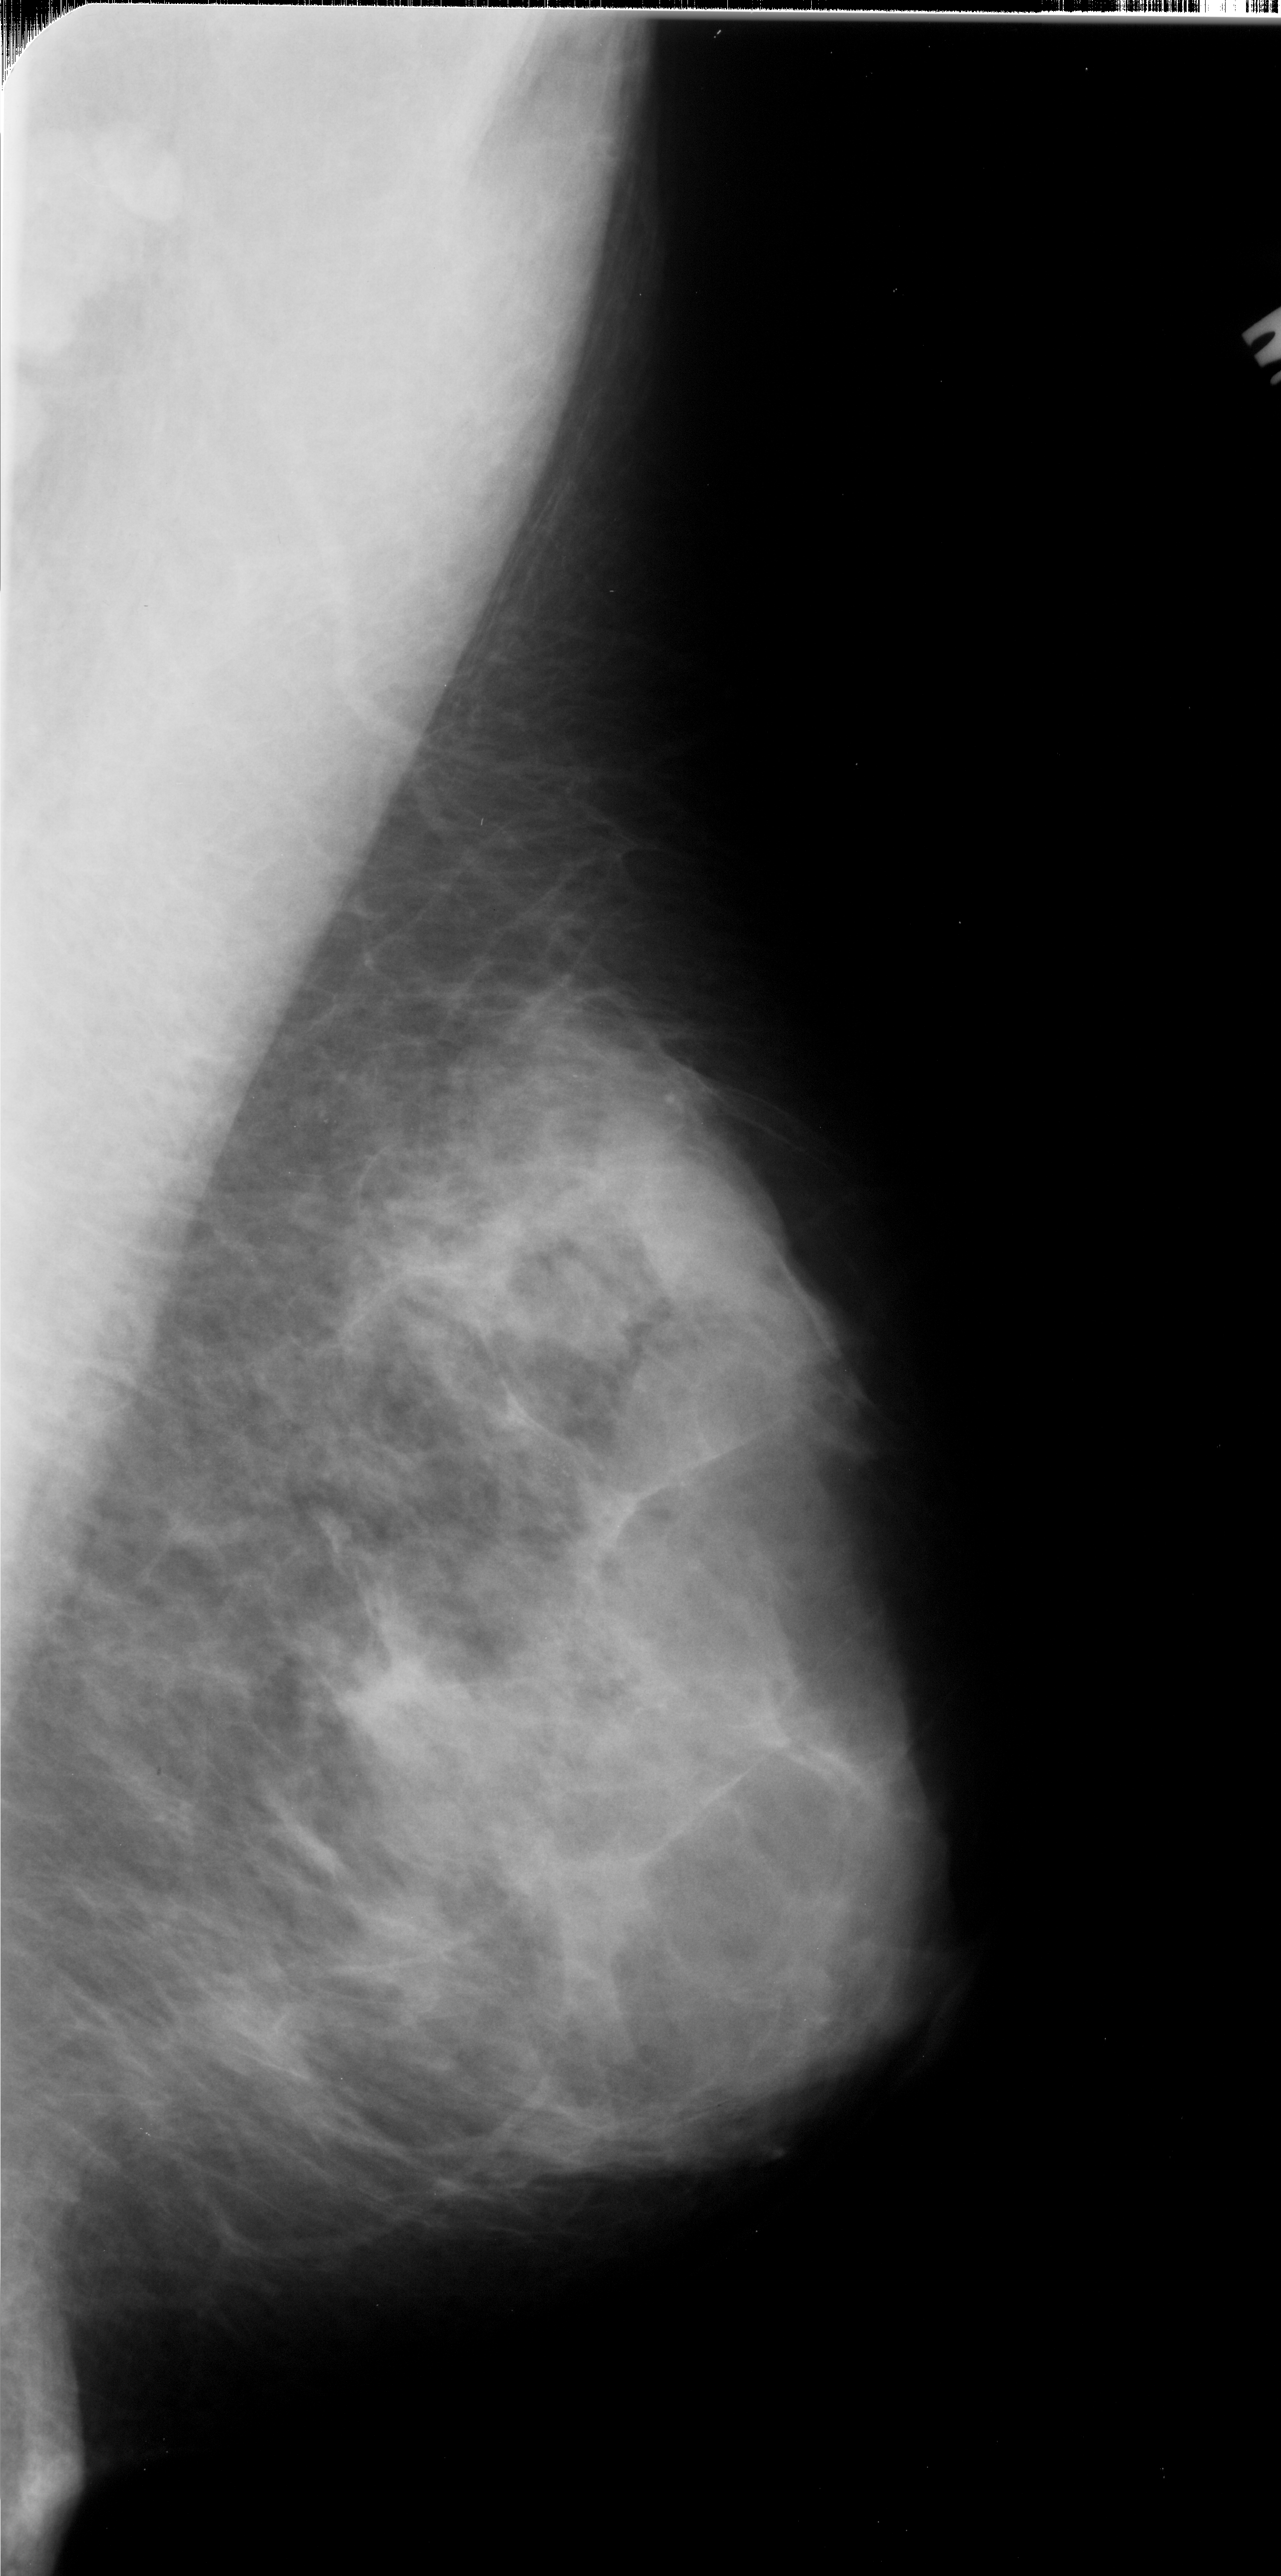
Mammogram (digitized film); right breast; mediolateral oblique (MLO) view; BI-RADS breast density category 4 (scale 1–4).
Finding: calcifications, morphology pleomorphic, distribution clustered; BI-RADS assessment category 4; pathology (as recorded): malignant.